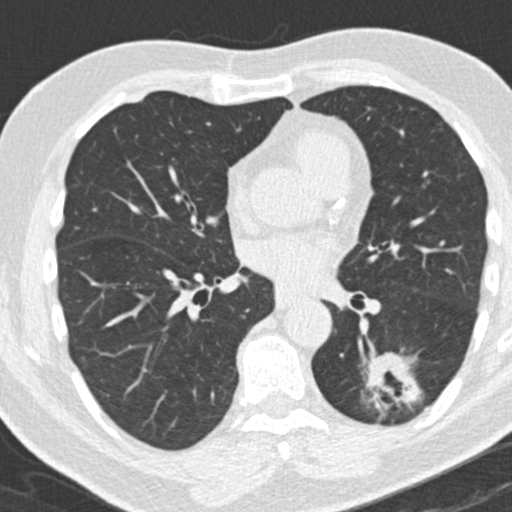
Low-dose screening chest CT, one axial slice. Position 95 of 180 along the scan axis. Reconstruction kernel B30f. Lung window (W 1500 / L -600 HU). 512 × 512 image matrix.
Structures marked on this image (expert manual segmentation):
- lesion 1 (tumor, lower lobe of left lung): bounding box (x1, y1, x2, y2) in pixels: (368, 353, 420, 396)